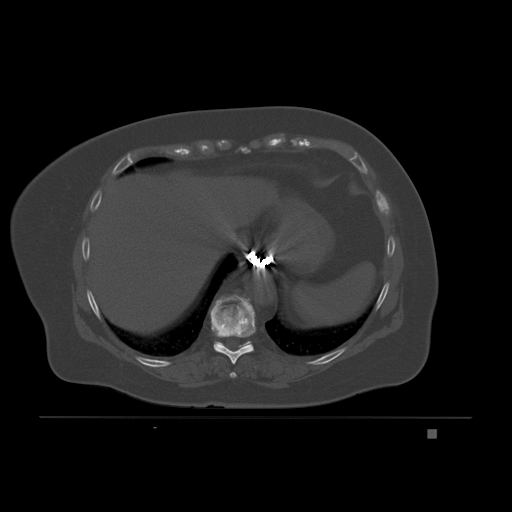
CT including the spine, one axial slice. Position 107 of 221 along the scan axis. Bone window (W 1800 / L 400 HU). 3 mm slice thickness. 512 × 512 image matrix, field of view 474 × 474 mm. Female patient, age 63 years. From the clinical record (not read from this slice): primary cancer: breast.
Outlined on this slice (semi-automatically segmented with operator editing):
- T10 vertebra: bounding box [x1, y1, x2, y2] px = [214, 341, 251, 348]
- T8 vertebra: [229, 372, 237, 378]
- T9 vertebra: [210, 301, 255, 364]